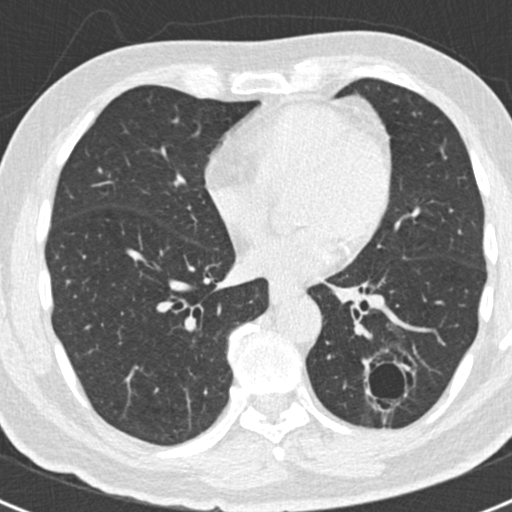
Chest CT (low-dose screening protocol), one axial image, baseline screening round, lung window (W 1500 / L -600 HU), 2 mm slice thickness. Male participant, aged 66 years at enrolment. Former smoker at enrolment.
Expert reader's lesion annotation, box from (x=344, y=340) to (x=420, y=419) px. Screening reader's record for this exam (one nodule recorded; not confirmed to be the boxed lesion): non-calcified nodule or mass ≥4 mm, left lower lobe, 43 × 27 mm, smooth margins.